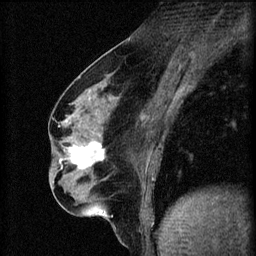
Breast MRI (dynamic contrast-enhanced), one sagittal slice. 3 images stored at this slice position (order not interpretable as contrast timing). 1.5 T. TE 4.2 ms, TR 8.2 ms. 2 mm slice thickness. 256 × 256 image matrix, field of view 180 × 180 mm. Female patient, age 56 years.
Structures marked on this image (semi-automatic segmentation, software-assisted and operator-edited):
- analysis volume of interest (the breast-tissue region the enhancement analysis was run in; not a lesion): bounding box [x1, y1, x2, y2] px = [62, 136, 111, 179]
- tumour enhancement mask (voxels above the 70 % enhancement threshold inside the analysis volume of interest): [68, 136, 104, 169]